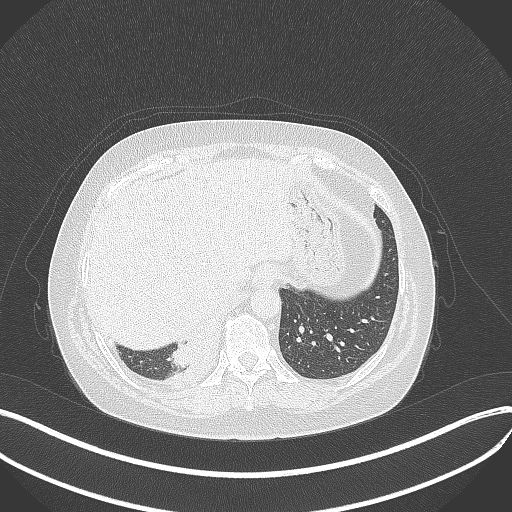
Chest CT, one axial slice. Position 77 of 381 along the scan axis. 120 kVp. Lung window (W 1500 / L -600 HU). 1 mm slice thickness. 512 × 512 image matrix. Female patient, age 56 years. Case-level facts recorded for this patient, not image findings: clinical TNM (as recorded): T2b N1 M0.
Annotated regions visible in this slice (rectangle marked by the reading radiologist):
- lung tumour (recorded histology: small cell carcinoma): box from (x=165, y=332) to (x=223, y=371) px